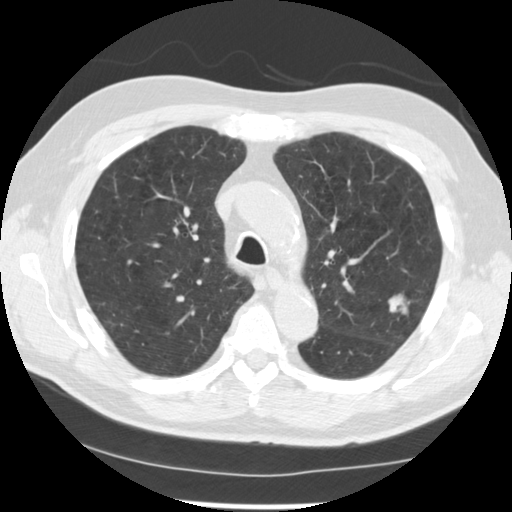
Axial slice from a low-dose chest CT screening exam; baseline annual screen; lung window (W 1500 / L -600 HU); 2.5 mm slice thickness; slice 175 of 249 in the series; 512 × 512 image matrix, field of view 341 × 341 mm. Male participant, aged 71 years at enrolment. Current smoker at enrolment.
- Lesion marked by an expert reader, bounding box (x1, y1, x2, y2) in pixels: (376, 283, 426, 331).
- The screening reader recorded 2 non-calcified nodules or masses ≥4 mm on this exam (left upper lobe, left upper lobe); which of them this box marks is not recorded.
- Participant outcome: lung cancer diagnosed 37 days after this screen — adenocarcinoma, NOS, left upper lobe, poorly differentiated (G3), stage IIIB (AJCC 6th edition), 25 mm at pathology.